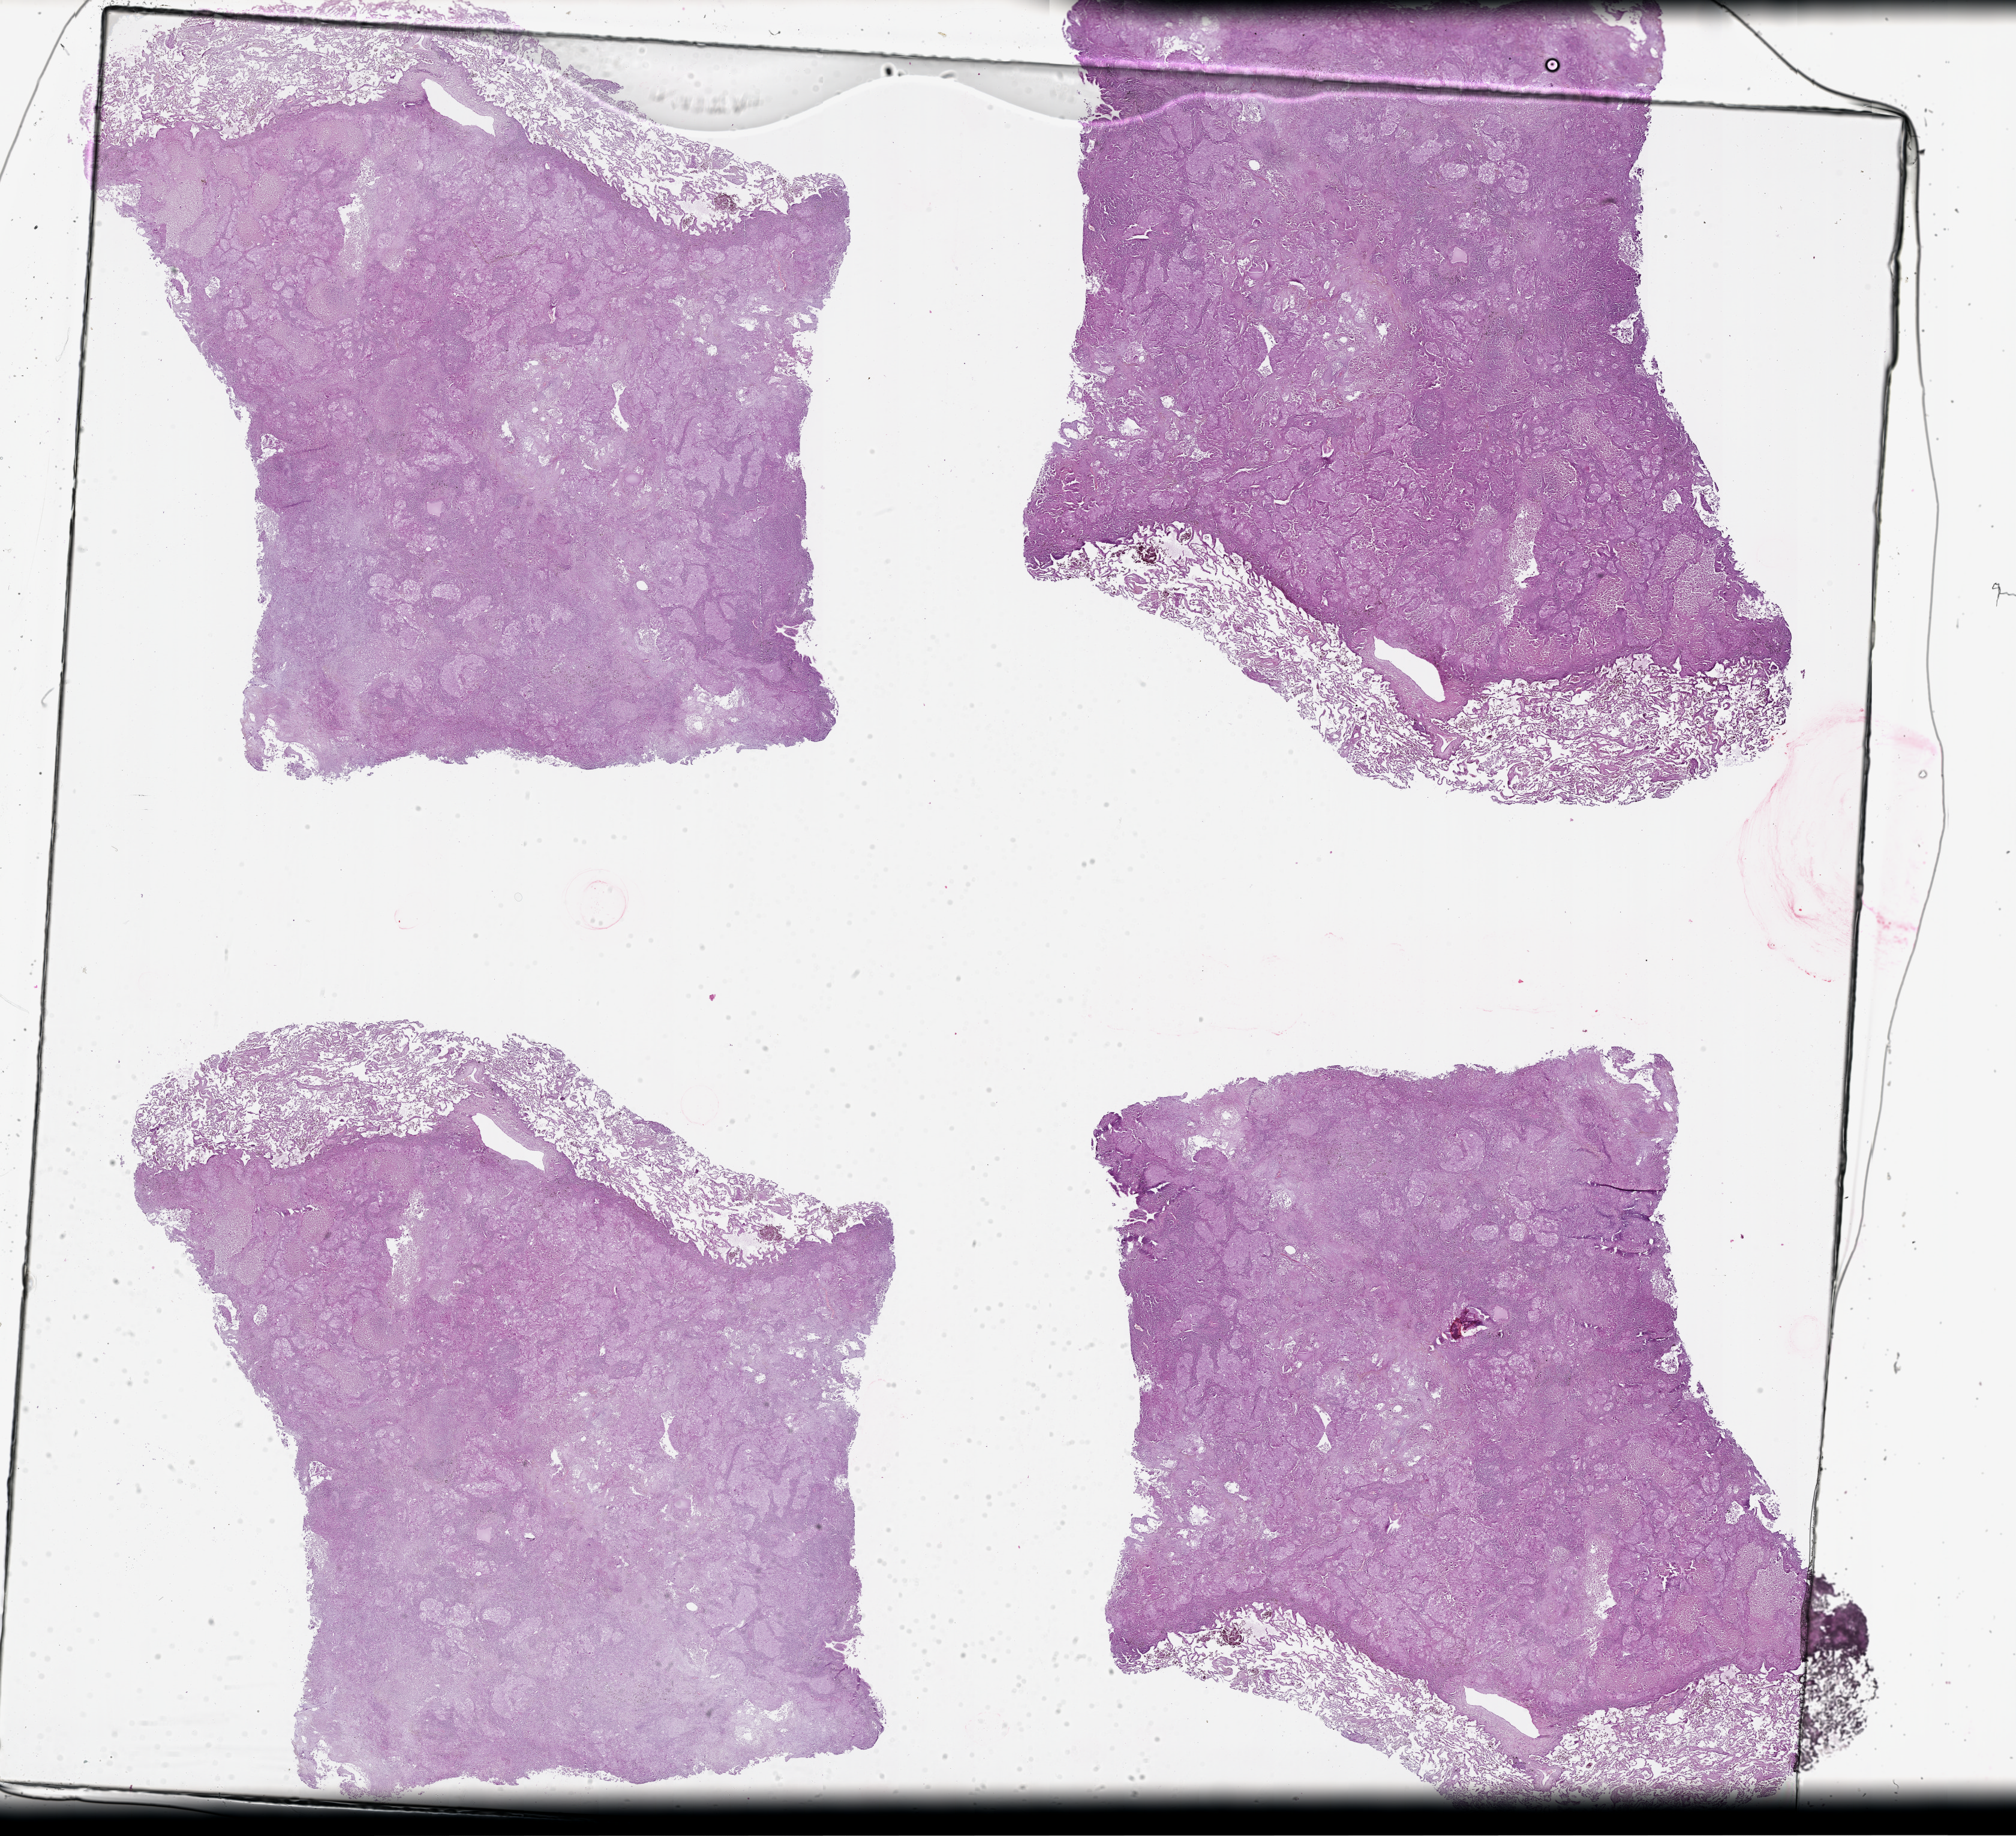
Whole-slide histology image, Hematoxylin and eosin (H&E) stained — a low-resolution overview of the entire scanned area, about 27.1 x 24.6 mm (from a 20x scan). Lung, tumour tissue. Male, 61 y/o.
Patient diagnosis (cohort enrolment): squamous cell carcinoma (lung).